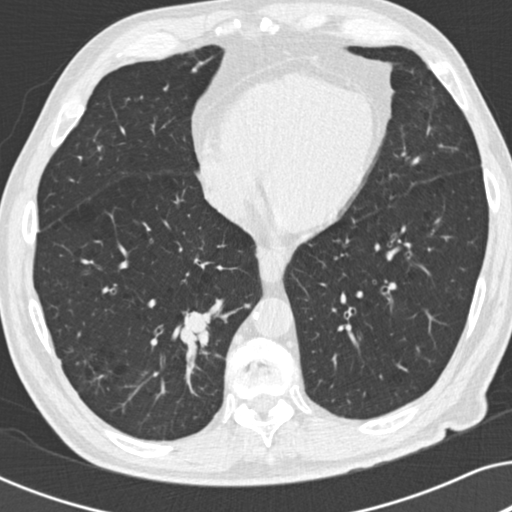
Low-dose screening chest CT, axial slice. Baseline annual screen. Lung window (W 1500 / L -600 HU). Standard (soft-tissue) reconstruction kernel (B30f). Slice 111 of 191 in the series. Male, age 73 years at enrolment. Current smoker at enrolment.
Lesion marked by an expert reader, bounding box (x1, y1, x2, y2) in pixels: (157, 294, 226, 367). The screening reader recorded 2 non-calcified nodules or masses ≥4 mm on this exam (right lower lobe, right upper lobe); which of them this box marks is not recorded.